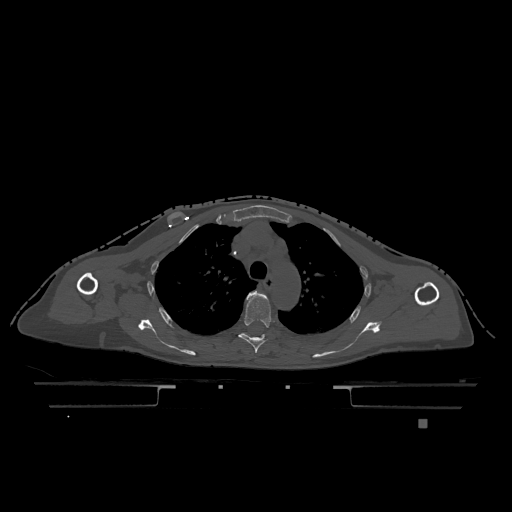
CT including the spine, one axial slice; position 879 of 1317 along the scan axis; bone window (W 1800 / L 400 HU); 512 × 512 image matrix, field of view 500 × 500 mm. Female patient, age 74 years. From the clinical record (not read from this slice): primary cancer: lung.
Annotated regions visible in this slice (semi-automatic segmentation, software-assisted and operator-edited):
- T4 vertebra: bounding box (x1, y1, x2, y2) in pixels: (238, 291, 275, 353)